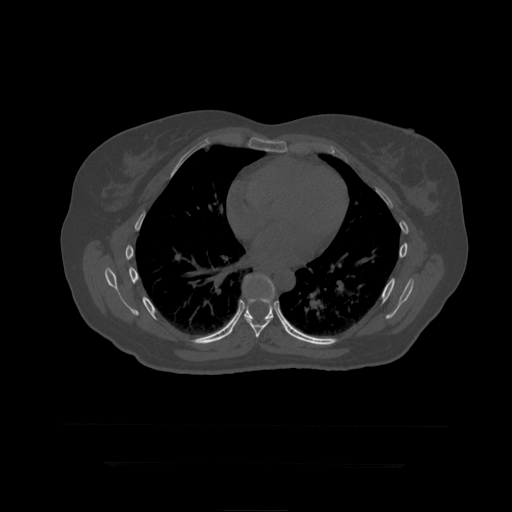
CT including the spine, one axial slice; slice 273 of 399 in the series (ordered by position); reconstruction kernel STANDARD; 120 kVp; bone window (W 1800 / L 400 HU); 1.25 mm slice thickness; 512 × 512 image matrix, field of view 450 × 450 mm. Patient age 41 years. Case-level facts recorded for this patient, not image findings: primary cancer: breast.
Outlined on this slice (semi-automatic segmentation, software-assisted and operator-edited):
- T8 vertebra: bounding box <244,276,272,338> (left, top, right, bottom; pixels)
- T9 vertebra: <230,274,290,335>